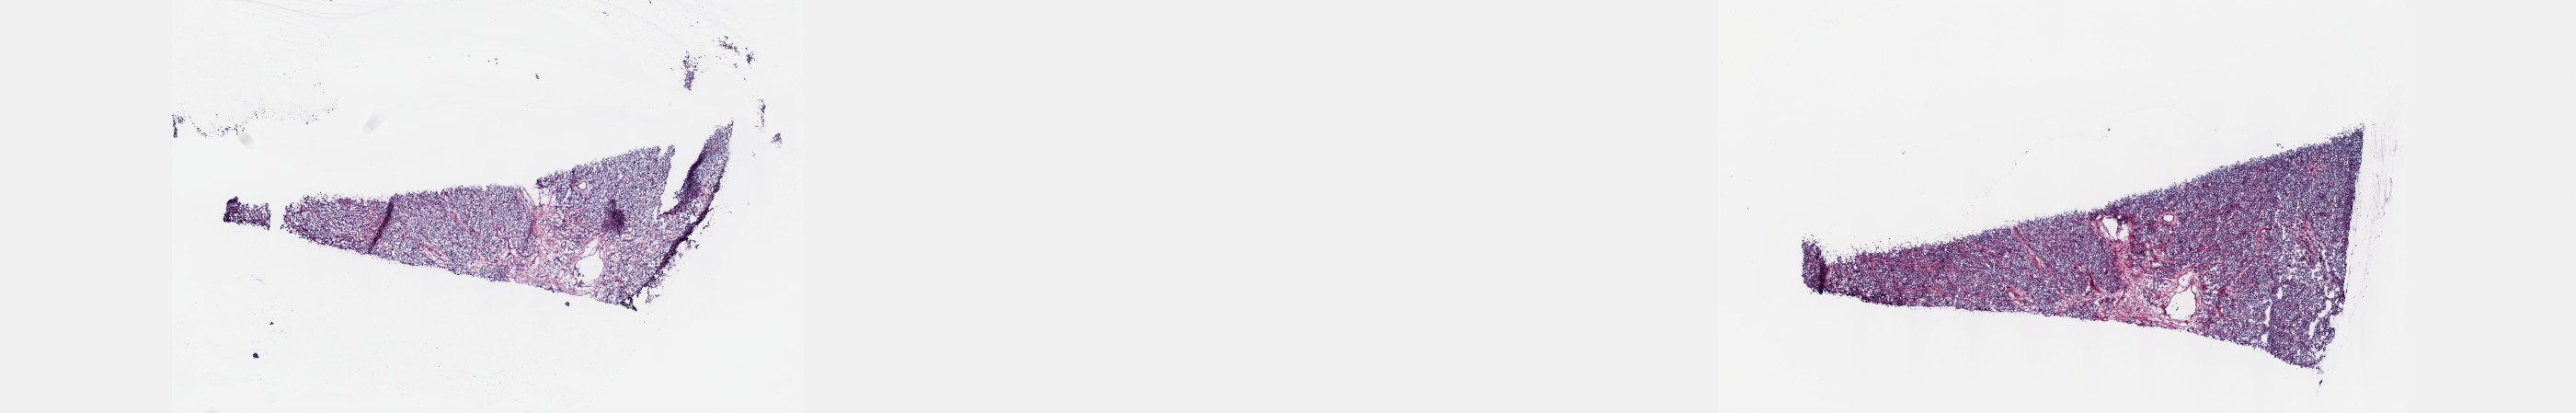
Whole-slide histology image, Hematoxylin and eosin (H&E) stained, whole scanned area (about 22.6 x 3.6 mm, from a 40x scan) shown as a low-resolution overview, frozen section from the top of the tissue portion, testis, additional new primary tumour sample. Patient sex: male. Composition of this section per pathologist review: tumour cells 90%, tumour nuclei 90%, normal cells 0%, stromal cells 10%, necrosis 0%. Infiltration values recorded for this section: lymphocyte infiltration 40%, monocyte infiltration 20%, neutrophil infiltration 20%.
This section: additional new primary tumour.